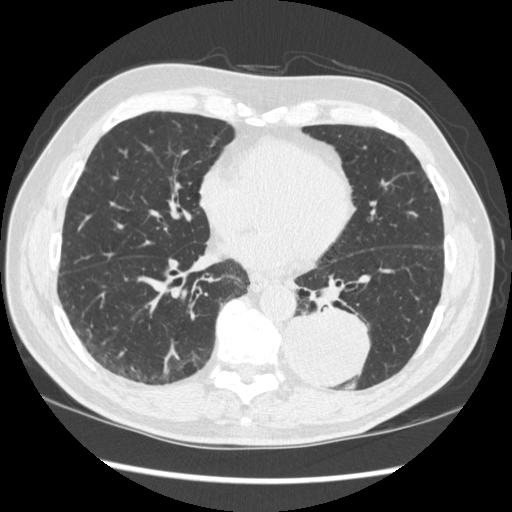
Chest CT (low-dose screening protocol), one axial image. First (baseline) screen. Lung window (W 1500 / L -600 HU). 120 kVp. 512 × 512 image matrix. Male participant, aged 72 years at enrolment. Current smoker at enrolment.
Expert reader's lesion annotation, bounding box <271,299,375,389> (left, top, right, bottom; pixels). The screening reader recorded 2 non-calcified nodules or masses ≥4 mm on this exam; which of them this box marks is not recorded. Later outcome: lung cancer diagnosed 37 days after this screen — squamous cell carcinoma, NOS, left lower lobe, stage IIIA (AJCC 6th edition), 60 mm at pathology.